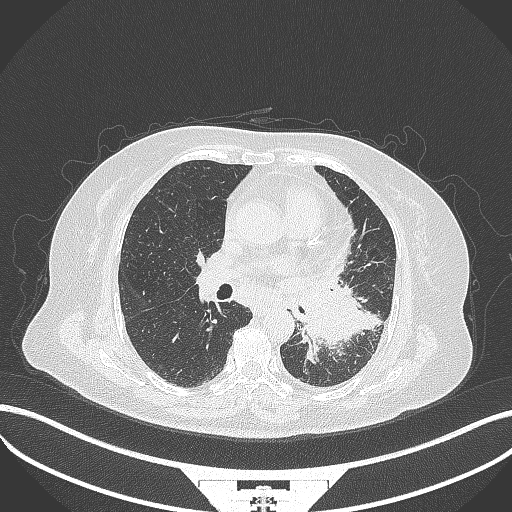
Chest CT, one axial slice. Reconstruction kernel B70f. Lung window (W 1500 / L -600 HU). 1 mm slice thickness. 512 × 512 image matrix, field of view 400 × 400 mm. Patient: female, 69 years. Case-level facts recorded for this patient, not image findings: clinical TNM (as recorded): T2b N3 M1.
Annotated regions visible in this slice (bounding box drawn by a radiologist):
- lung tumour (recorded histology: adenocarcinoma): box from (x=292, y=277) to (x=368, y=349) px